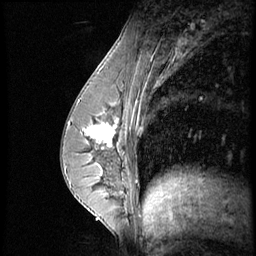
Breast MRI (dynamic contrast-enhanced), one sagittal slice; position 25 of 56 along the scan axis; dynamic contrast-enhanced series, image 2 of 4 at this slice position (ordered by acquisition); 1.5 T; TE 4.2 ms, TR 8.9 ms; 256 × 256 image matrix, field of view 200 × 200 mm. Patient: female, 35 years. Case-level facts recorded for this patient, not image findings: setting: breast cancer imaged before/during neoadjuvant chemotherapy; receptor status: HER2-positive.
Outlined on this slice (semi-automatically segmented with operator editing):
- analysis volume of interest (the breast-tissue region the enhancement analysis was run in; not a lesion): box from (x=73, y=111) to (x=131, y=164) px
- tumour enhancement mask (voxels above the 140 % enhancement threshold inside the analysis volume of interest): (x=78, y=120)–(x=119, y=164)